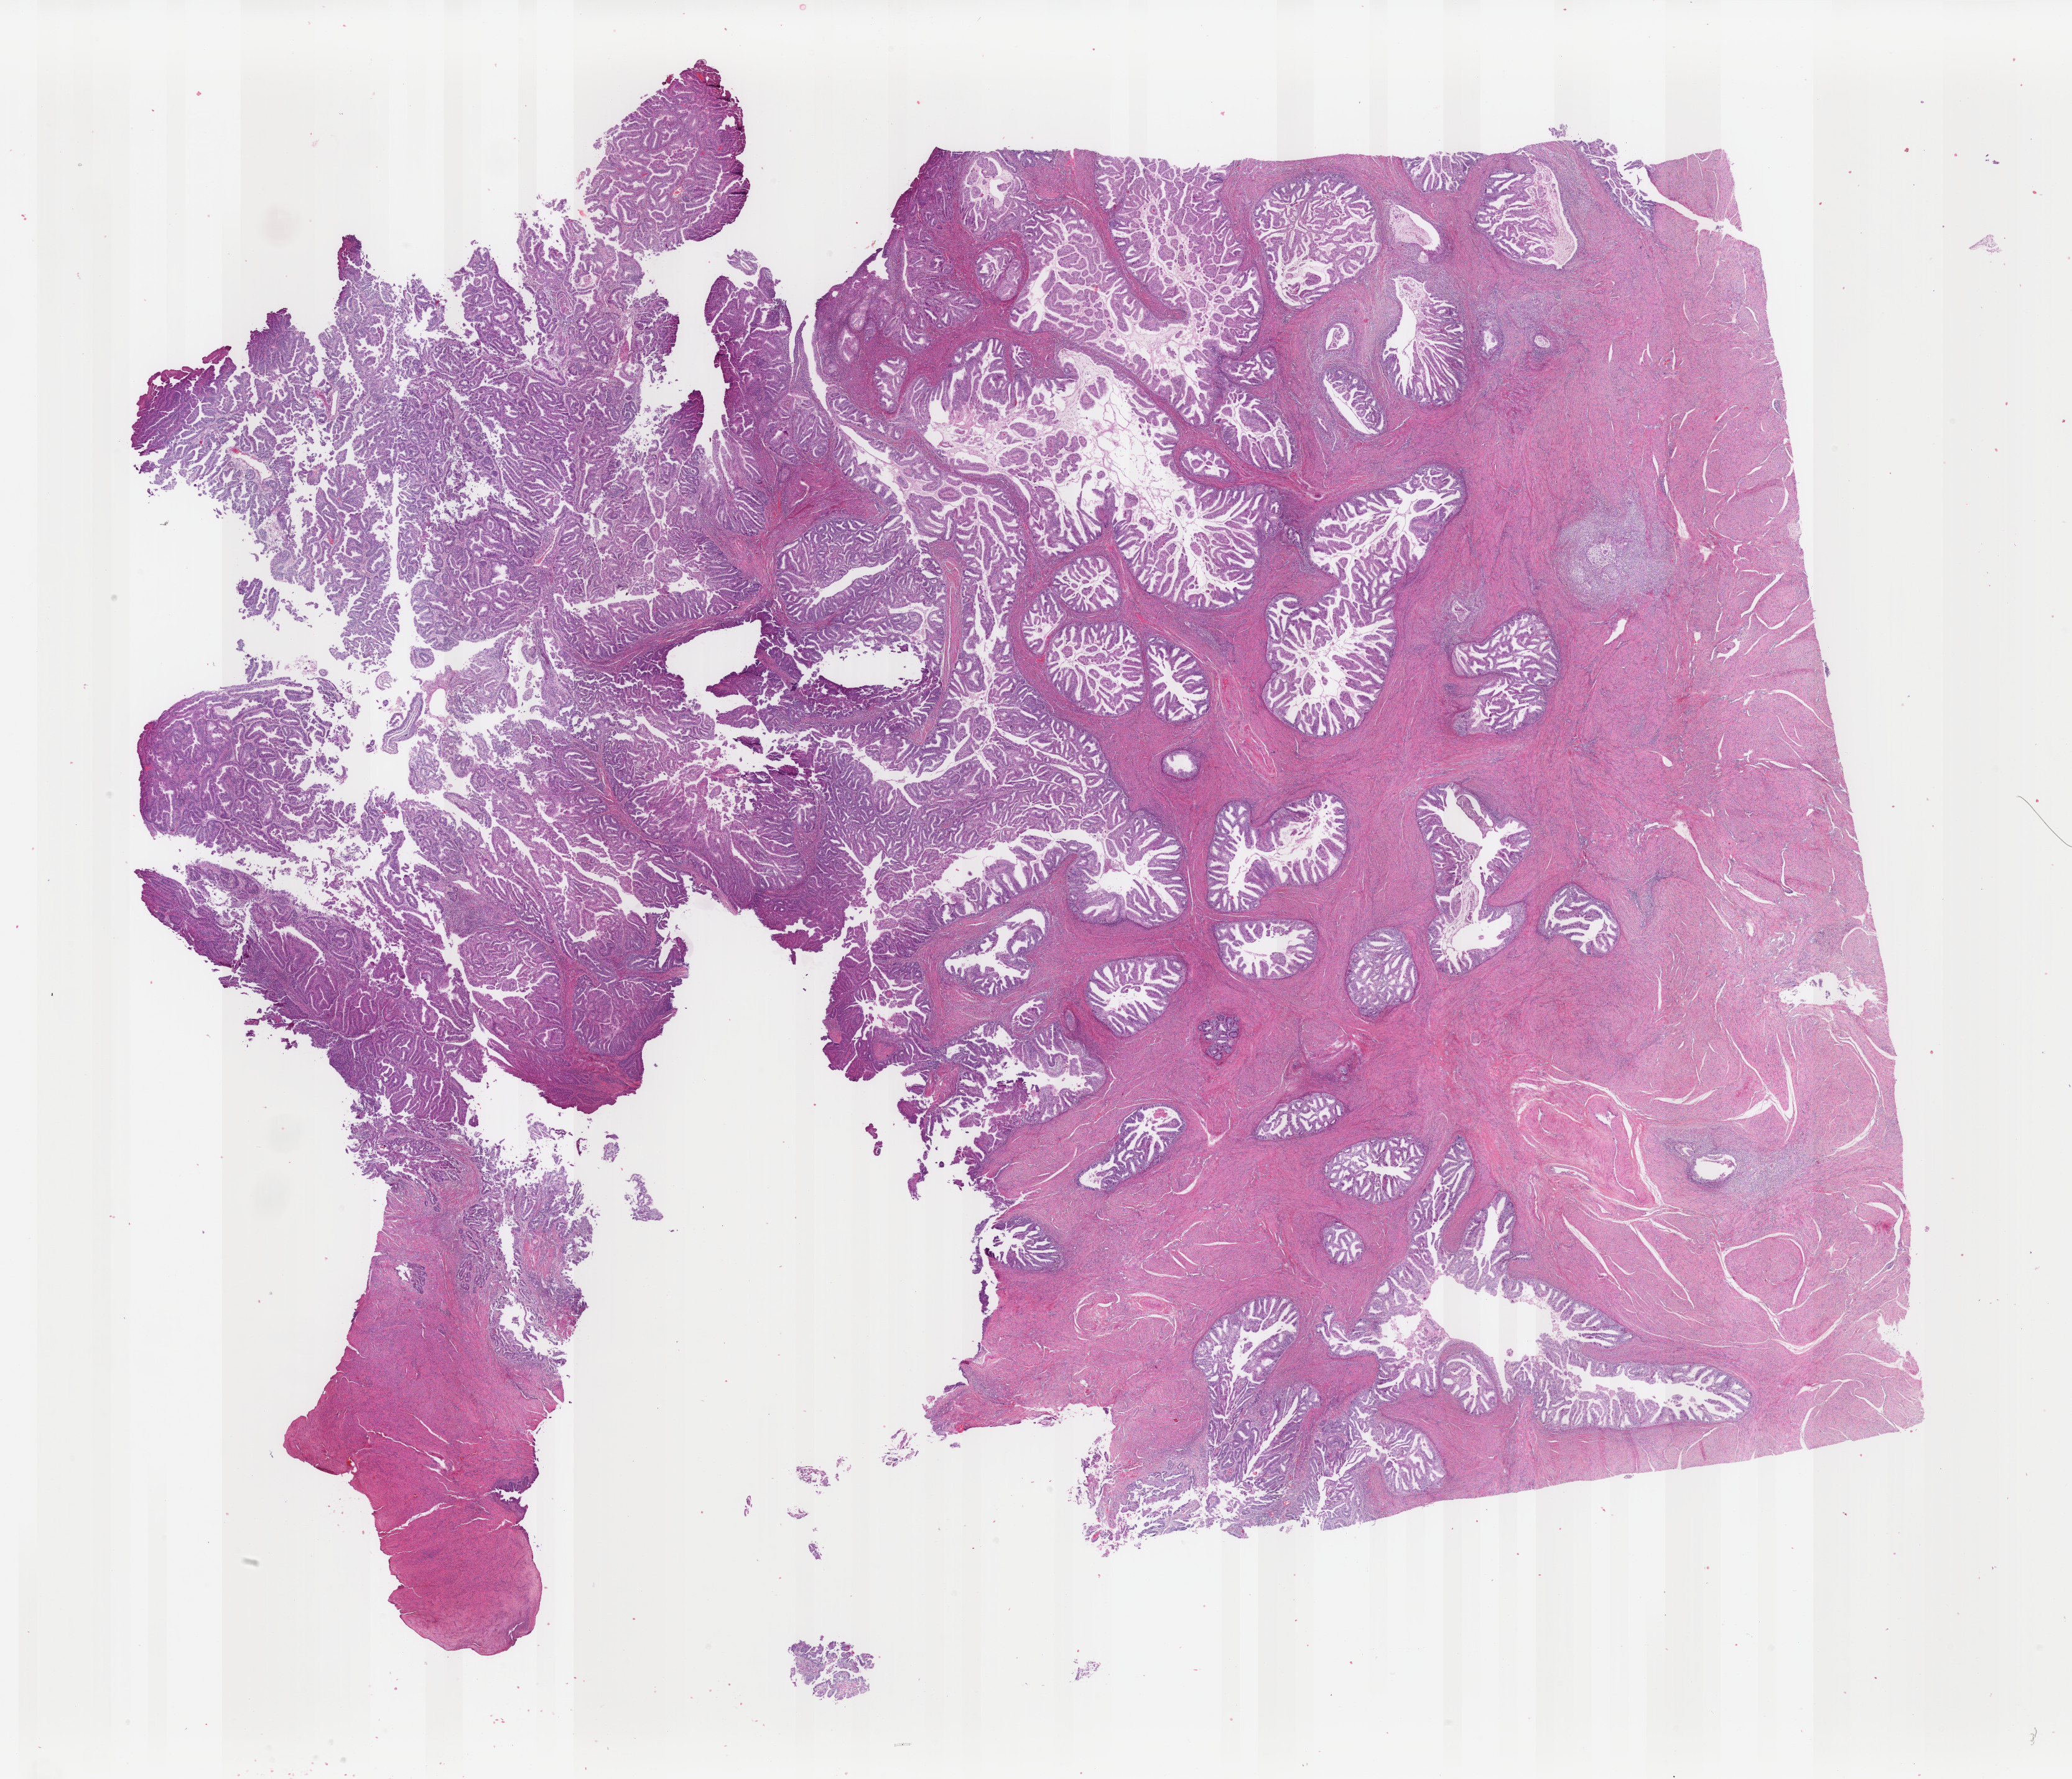
Digitized H&E-stained tissue section (whole slide) — a low-resolution overview of the entire scanned area, about 26.4 x 22.7 mm; formalin-fixed paraffin-embedded (FFPE) diagnostic section; uterus, primary tumour sample. Patient: female, age at initial diagnosis 61 years. Histologic grade: G2 (moderately differentiated).
* FIGO stage: IB
* diagnosis: Endometrioid adenocarcinoma, NOS (endometrium)